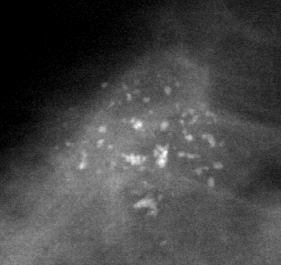
Cropped region of a digitized screen-film mammogram centred on a radiologist-marked abnormality; right breast; MLO view; BI-RADS breast density category 3 (scale 1–4).
Marked abnormality: calcifications, morphology pleomorphic, distribution clustered; BI-RADS assessment category 5; pathology result (as recorded, not read from the image): malignant.